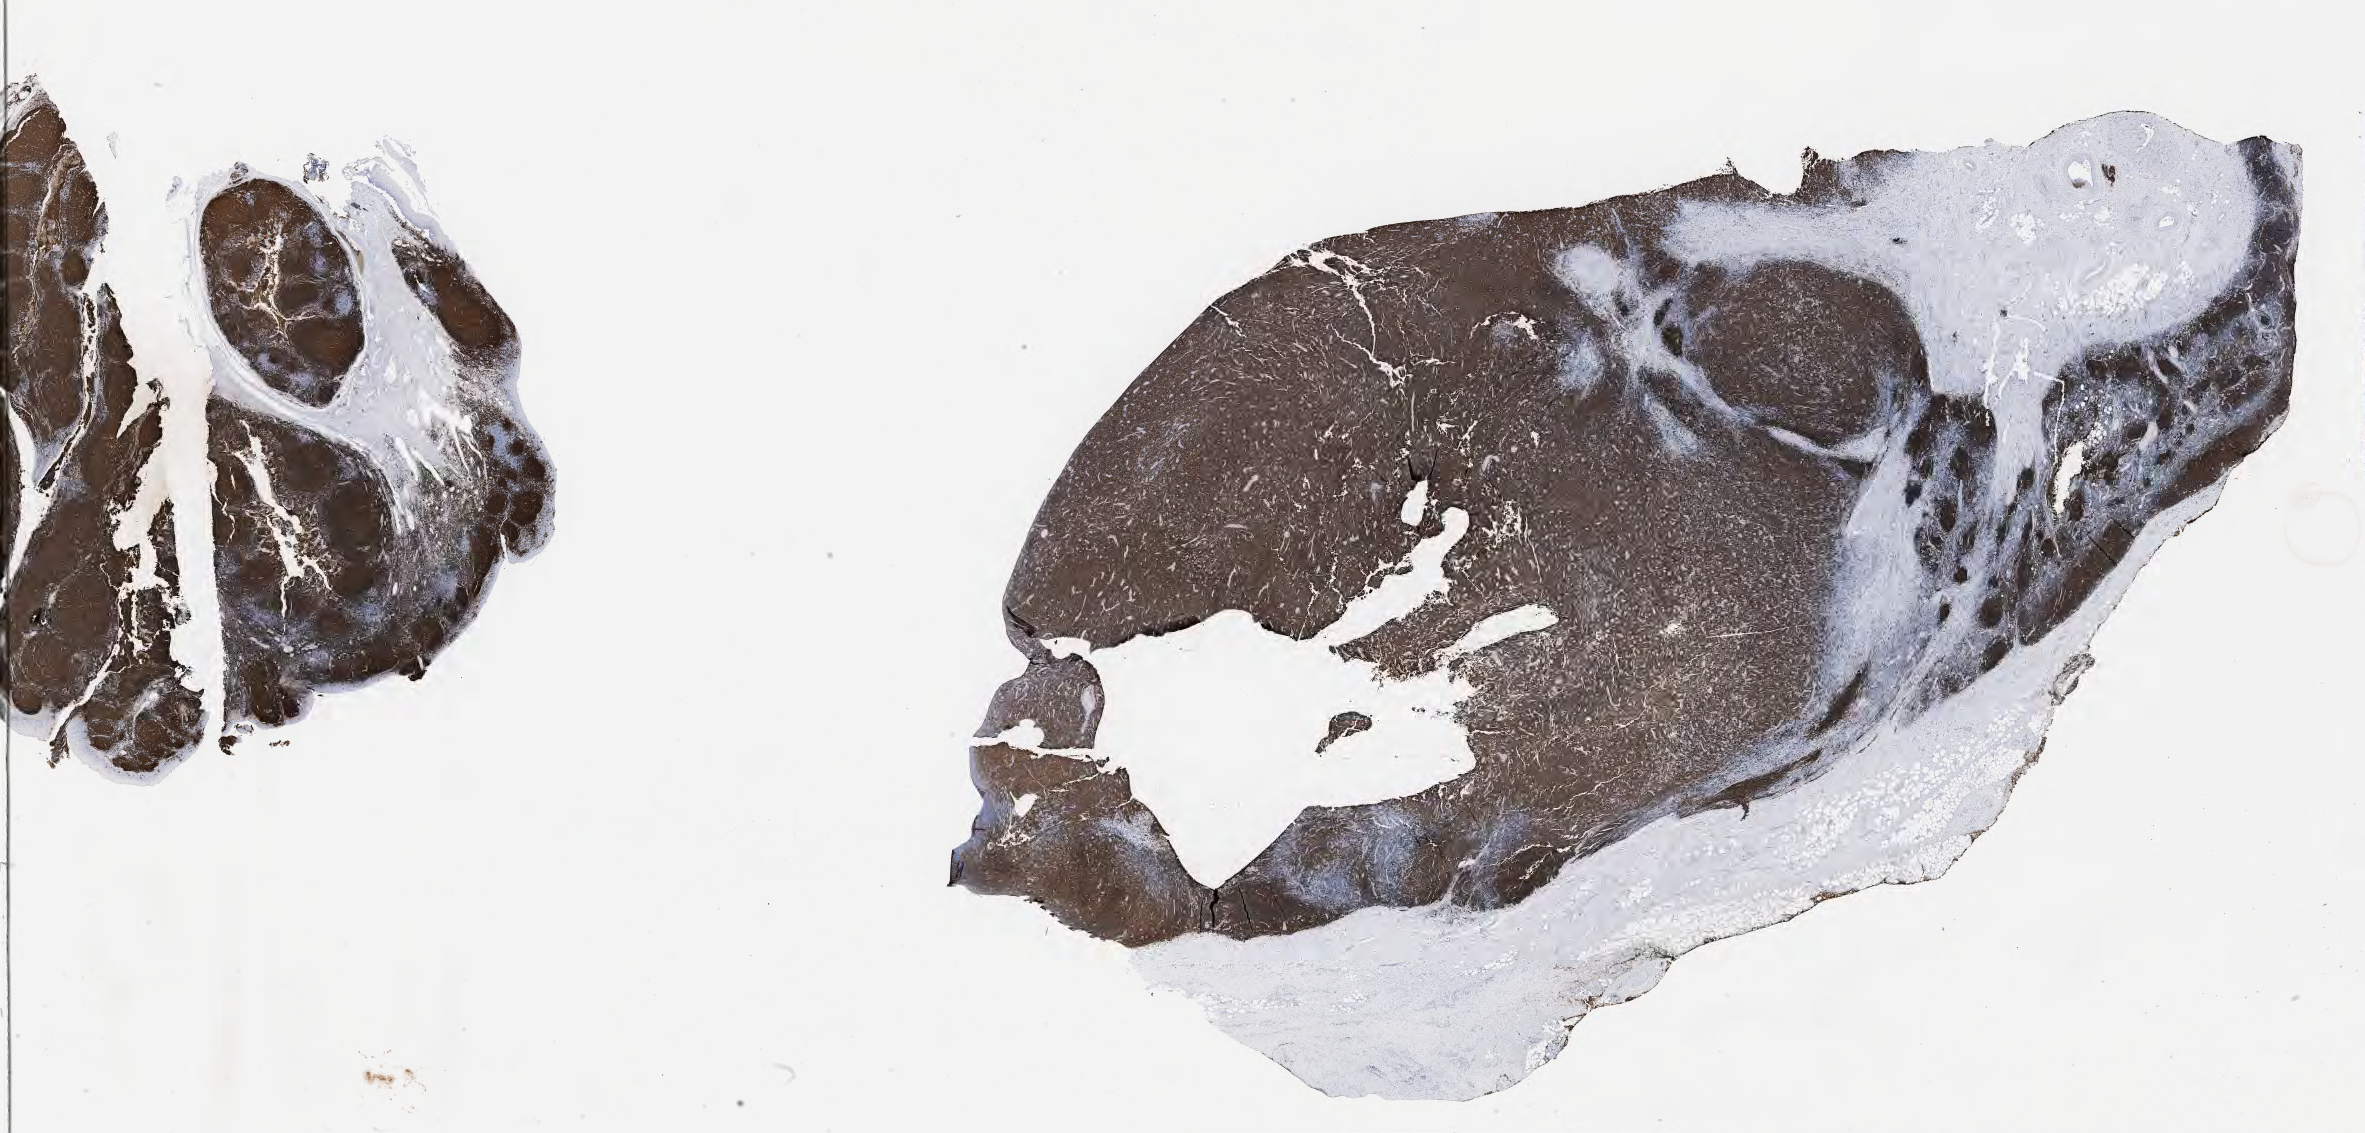
Whole-slide image, immunohistochemical stain for CD20 — a low-resolution overview of the entire scanned area, about 38.2 x 18.3 mm; specimen: tumor tissue; site: lymph node. Male patient, age 60 years.
Histologic diagnosis: Diffuse large B-cell lymphoma, NOS.